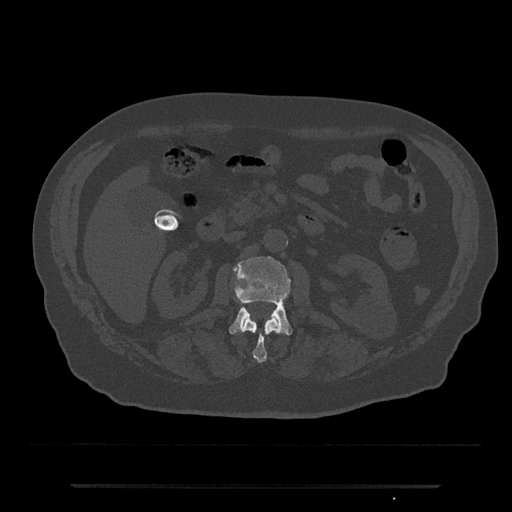
CT including the spine, one axial slice. Reconstruction kernel Br40s/3. Bone window (W 1800 / L 400 HU). 512 × 512 image matrix, field of view 434 × 434 mm. Patient: male, 80 years. Case-level facts recorded for this patient, not image findings: primary cancer: prostate; vertebrae with lytic lesions (as recorded): L1, T11.
Outlined on this slice (semi-automatic segmentation, software-assisted and operator-edited):
- L1 vertebra: box from (x=243, y=317) to (x=280, y=363) px
- L2 vertebra: (x=229, y=256)–(x=293, y=335)